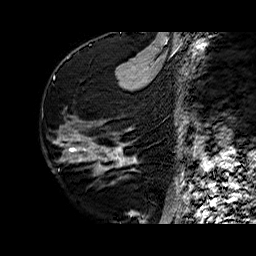
Breast MRI (dynamic contrast-enhanced), one sagittal slice; position 22 of 60 along the scan axis; dynamic contrast-enhanced series, time point 2 of 6 at this slice position (early post-contrast); 1.5 T; TE 6.4 ms, TR 32.7 ms; 4 mm slice thickness; 256 × 256 image matrix, field of view 200 × 200 mm. Female patient. From the clinical record (not read from this slice): setting: breast cancer imaged before/during neoadjuvant chemotherapy; receptor status: HR-positive, HER2-negative.
Outlined on this slice (semi-automatic segmentation, software-assisted and operator-edited):
- analysis volume of interest (the breast-tissue region the enhancement analysis was run in; not a lesion): bounding box (x1, y1, x2, y2) in pixels: (73, 116, 138, 175)
- tumour enhancement mask (voxels above the 100 % enhancement threshold inside the analysis volume of interest): (115, 148, 136, 164)